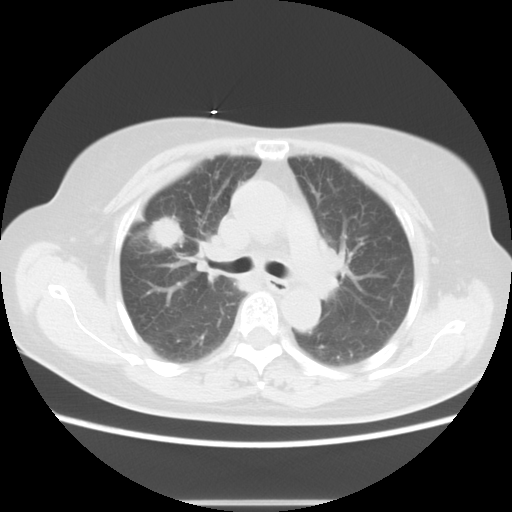
Chest CT, one axial slice; position 9 of 17 along the scan axis; reconstruction kernel STANDARD; 120 kVp; lung window (W 1500 / L -600 HU); 5 mm slice thickness; 512 × 512 image matrix, field of view 350 × 350 mm. Patient: female, 57 years. Case-level facts recorded for this patient, not image findings: clinical TNM (as recorded): T1c N1 M0.
Annotated regions visible in this slice (bounding box drawn by a radiologist):
- lung tumour (recorded histology: adenocarcinoma): bounding box <148,207,187,259> (left, top, right, bottom; pixels)